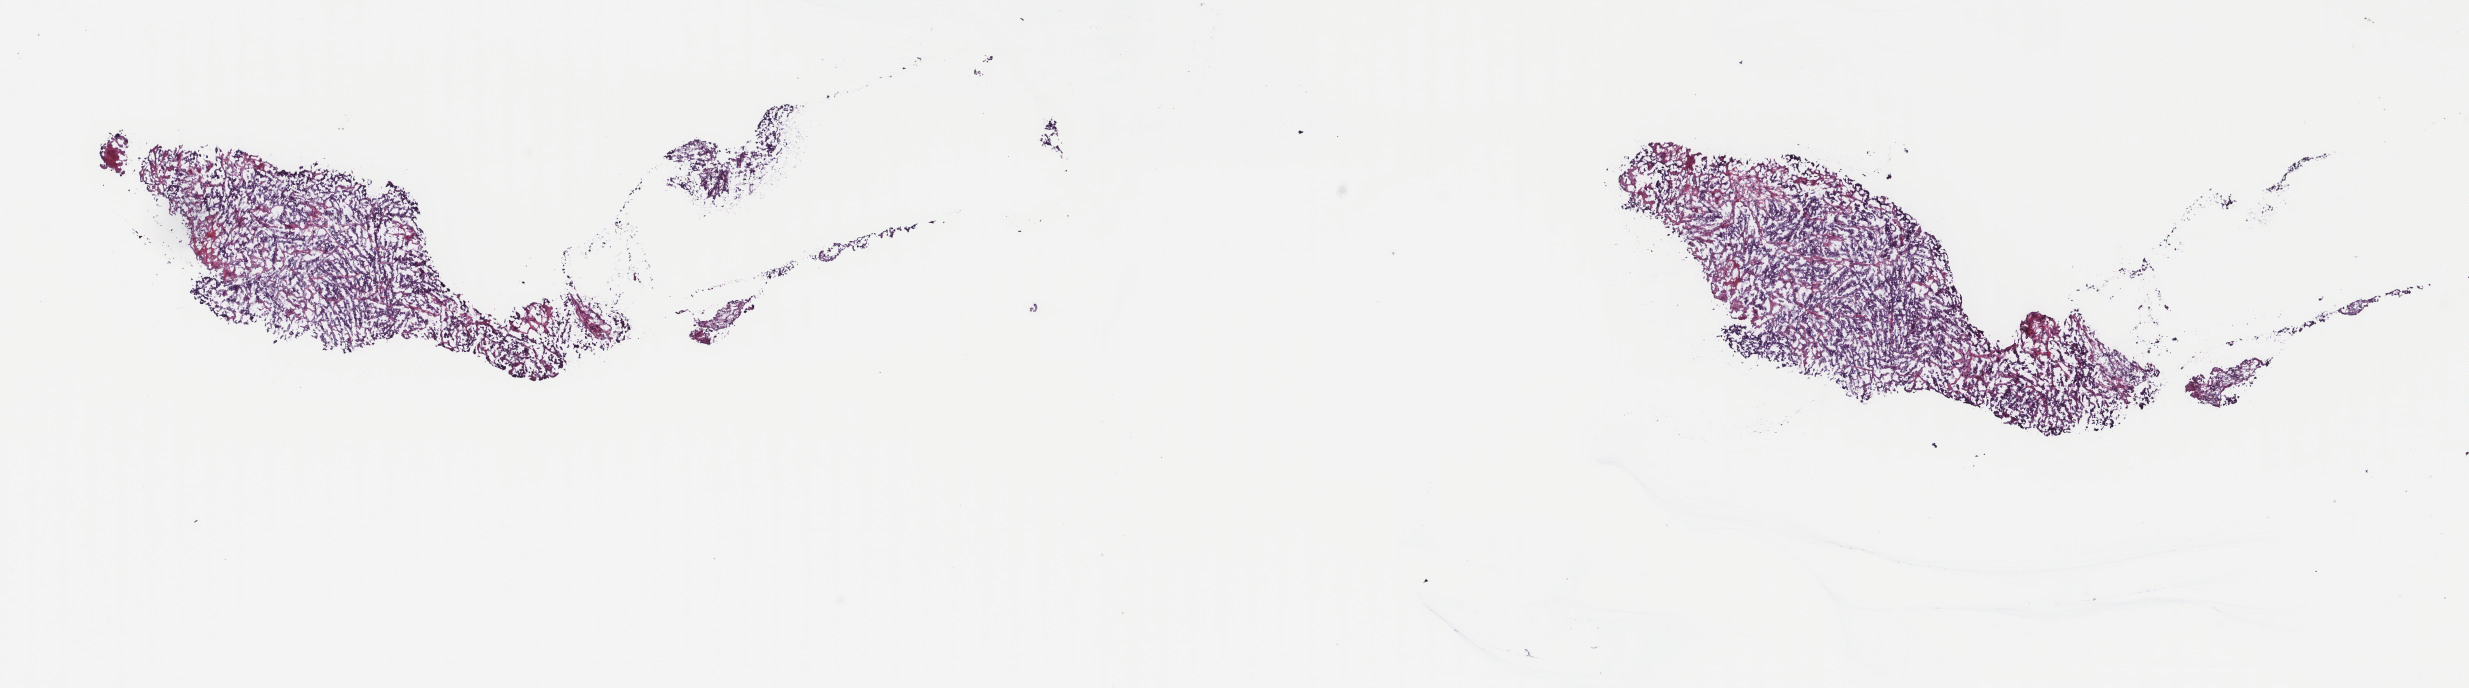
H&E whole-slide image, low-resolution overview of the scanned area, about 19.6 x 5.5 mm, frozen section, primary tumour sample from the bladder. Male patient; age at initial diagnosis 55 years. Histologic grade: high grade. Slide review estimates, as recorded: tumour cells 100%, tumour nuclei 90%, normal cells 0%, stromal cells 0%, necrosis 0%. Inflammatory infiltration, as recorded: lymphocyte infiltration 2%, monocyte infiltration 0%, neutrophil infiltration 0%.
* AJCC pathologic stage: IV
* lymph nodes positive (case pathology): 2 of 38 examined
* histologic diagnosis: Transitional cell carcinoma